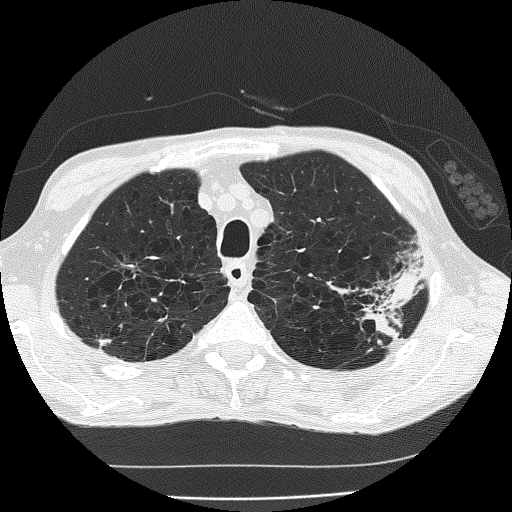
Axial slice from a low-dose chest CT screening exam, second annual screen, lung window (W 1500 / L -600 HU). Male participant, aged 60 years at enrolment. Current smoker at enrolment.
Expert-annotated lung lesion, bounding box <346,261,428,340> (left, top, right, bottom; pixels). The screening reader recorded 2 non-calcified nodules or masses ≥4 mm on this exam (left upper lobe, left upper lobe); which of them this box marks is not recorded. Official screen result: positive, other. Participant outcome: lung cancer diagnosed 178 days after this screen — bronchiolo-alveolar carcinoma, mucinous, left upper lobe, stage IV (AJCC 6th edition).